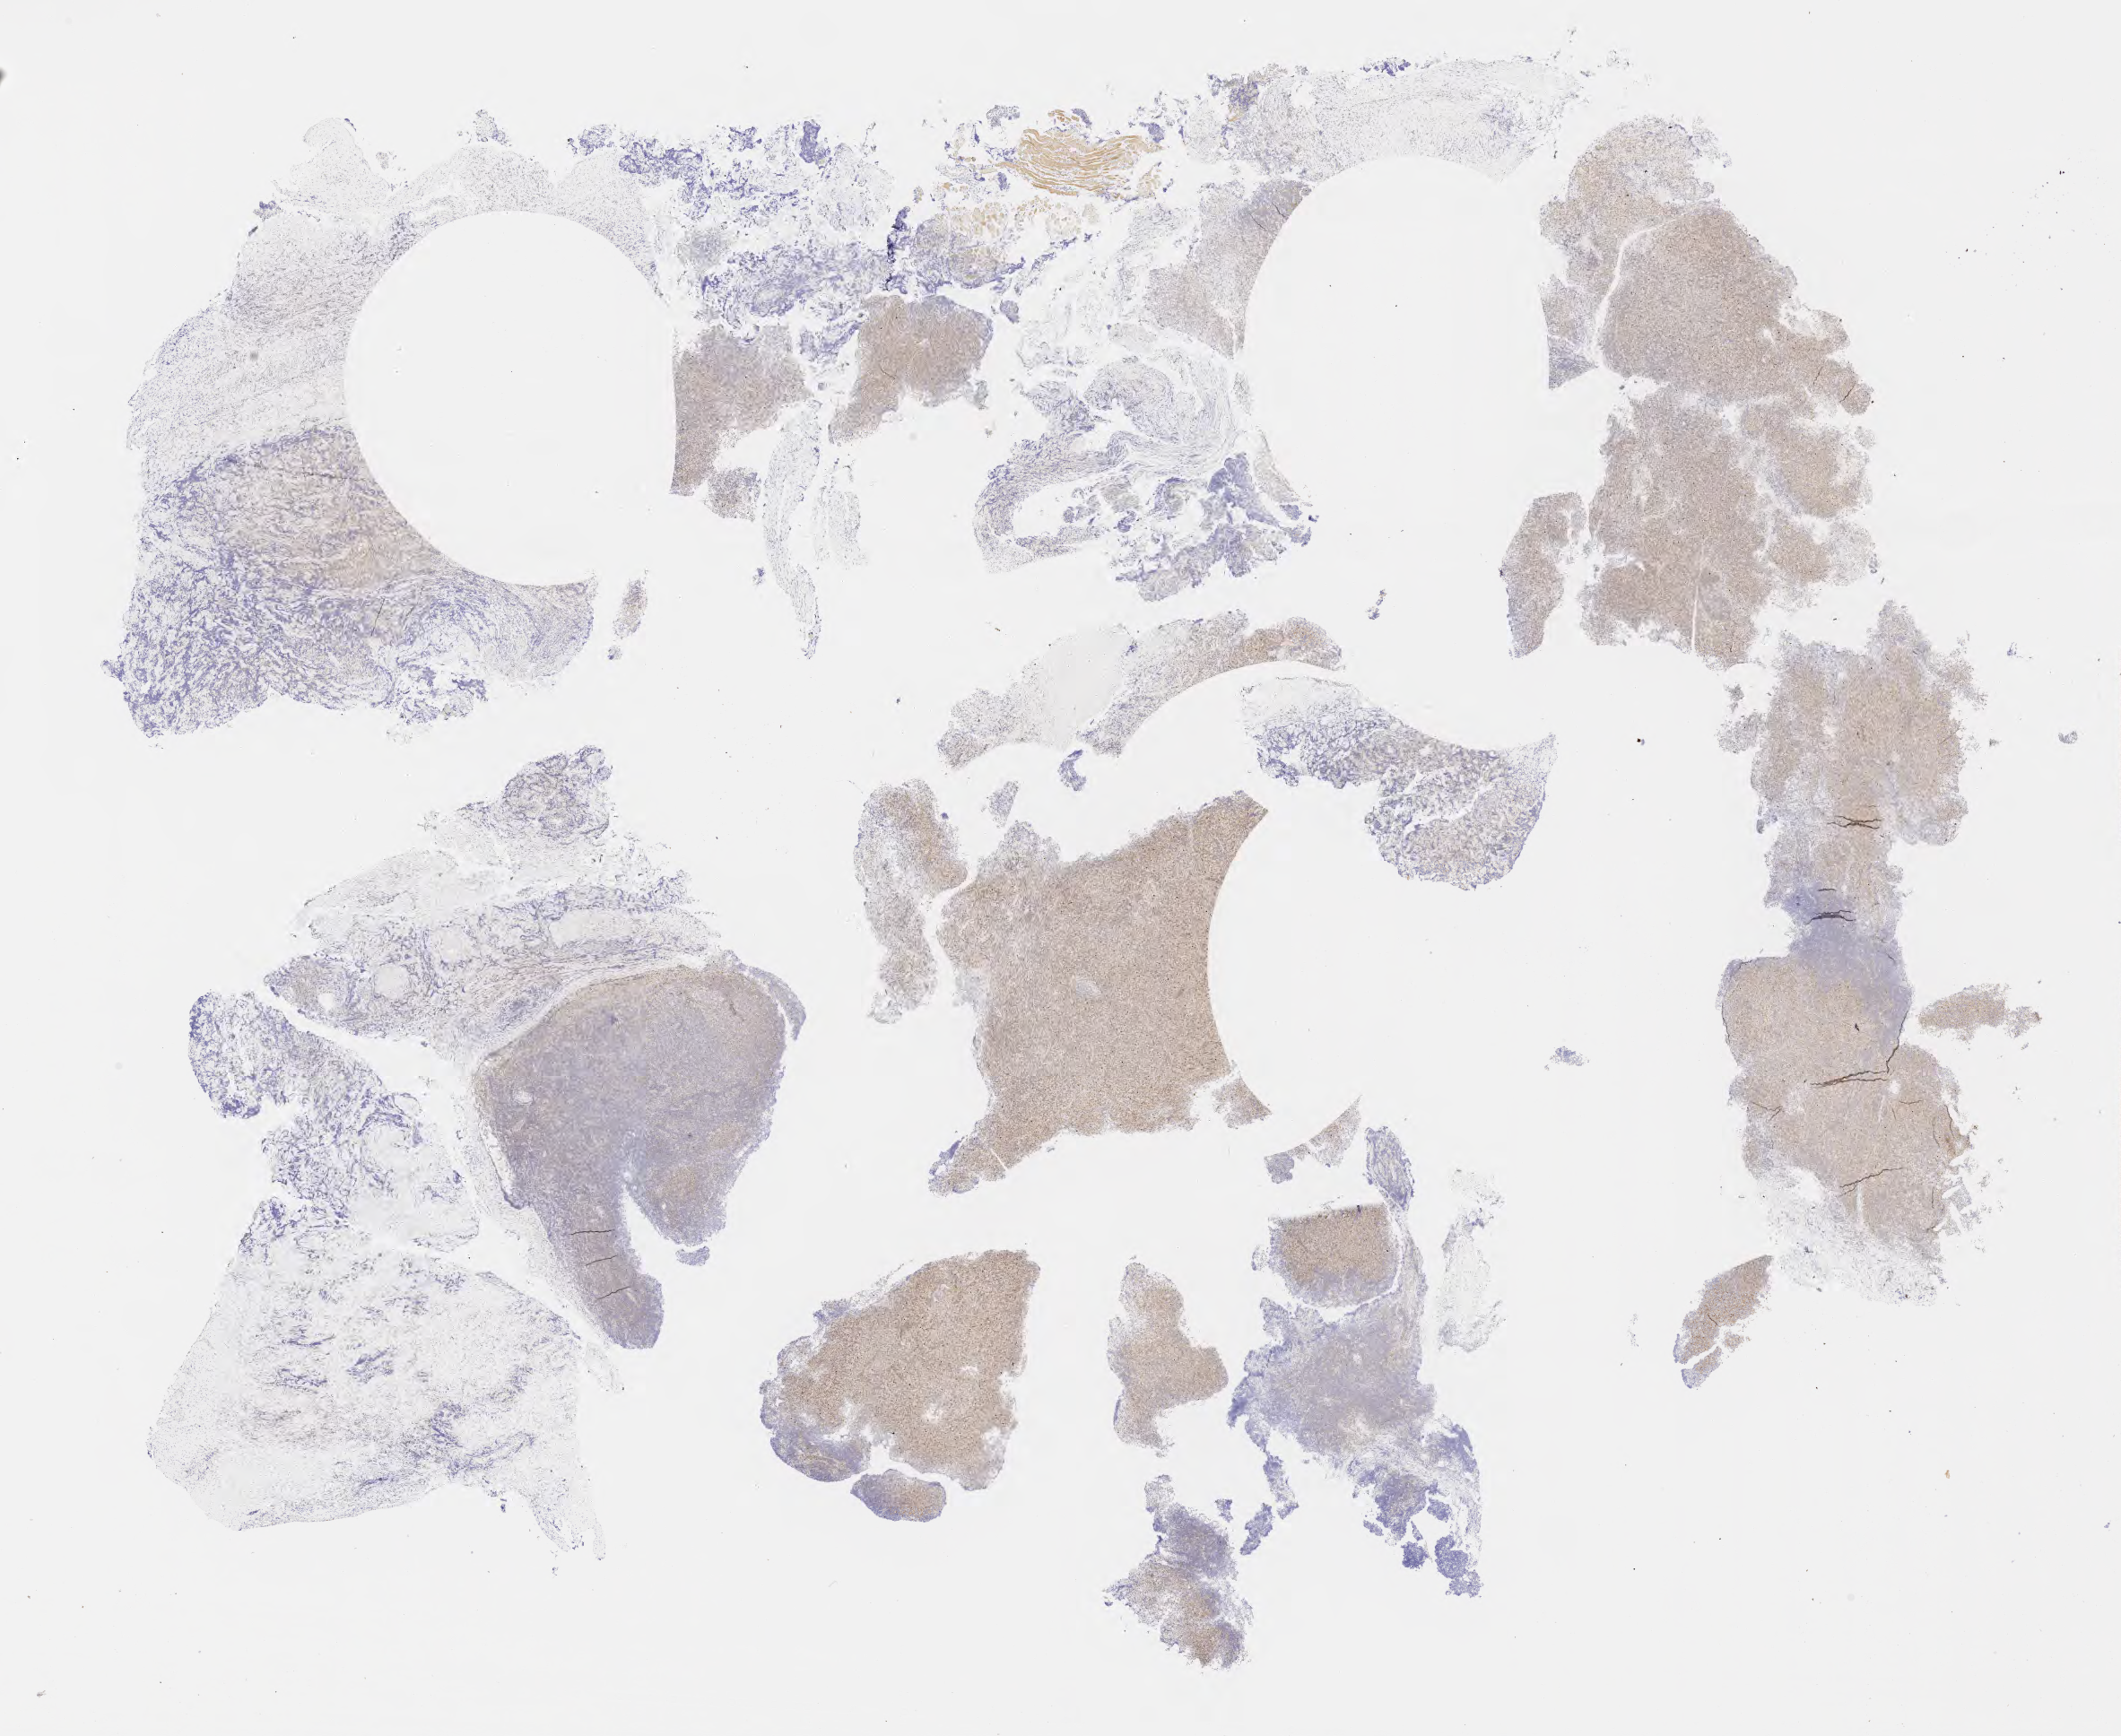
Immunohistochemistry (IHC) whole-slide image stained for p53 — low-resolution overview of the scanned area, about 19.1 x 15.7 mm; specimen: tumor tissue; site: lymph node. Patient male; 29 years old.
Histologic diagnosis: Diffuse large B-cell lymphoma, NOS.